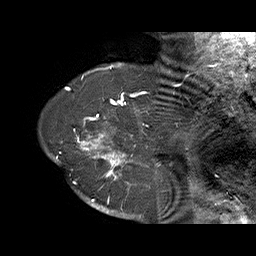
Breast MRI (dynamic contrast-enhanced), one sagittal slice. Position 58 of 70 along the scan axis. Dynamic contrast-enhanced series, time point 2 of 6 at this slice position (early post-contrast). 1.5 T. TE 4.5 ms, TR 32.4 ms. 256 × 256 image matrix, field of view 180 × 180 mm. Female patient. From the clinical record (not read from this slice): setting: breast cancer imaged before/during neoadjuvant chemotherapy; receptor status: HR-positive, HER2-negative.
Structures marked on this image (semi-automatically segmented with operator editing):
- analysis volume of interest (the breast-tissue region the enhancement analysis was run in; not a lesion): box from (x=71, y=128) to (x=159, y=202) px
- tumour enhancement mask (voxels above the 100 % enhancement threshold inside the analysis volume of interest): (x=71, y=128)–(x=159, y=202)